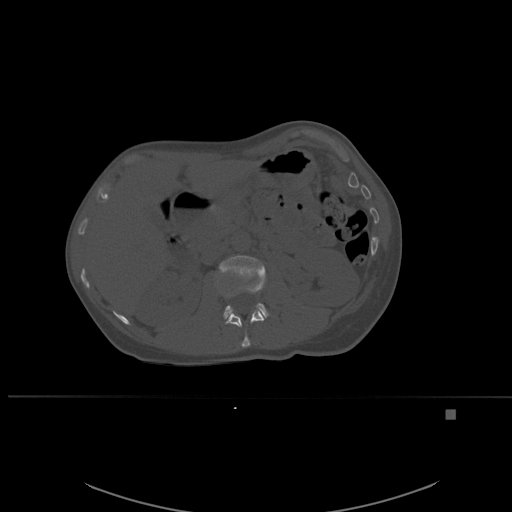
CT including the spine, one axial slice; position 248 of 537 along the scan axis; bone window (W 1800 / L 400 HU); 1.5 mm slice thickness; 512 × 512 image matrix, field of view 440 × 440 mm. Female patient, age 45 years. Case-level facts recorded for this patient, not image findings: primary cancer: lung.
Outlined on this slice (semi-automatic segmentation, software-assisted and operator-edited):
- L1 vertebra: bounding box (x1, y1, x2, y2) in pixels: (217, 280, 265, 348)
- L2 vertebra: (219, 255, 269, 319)